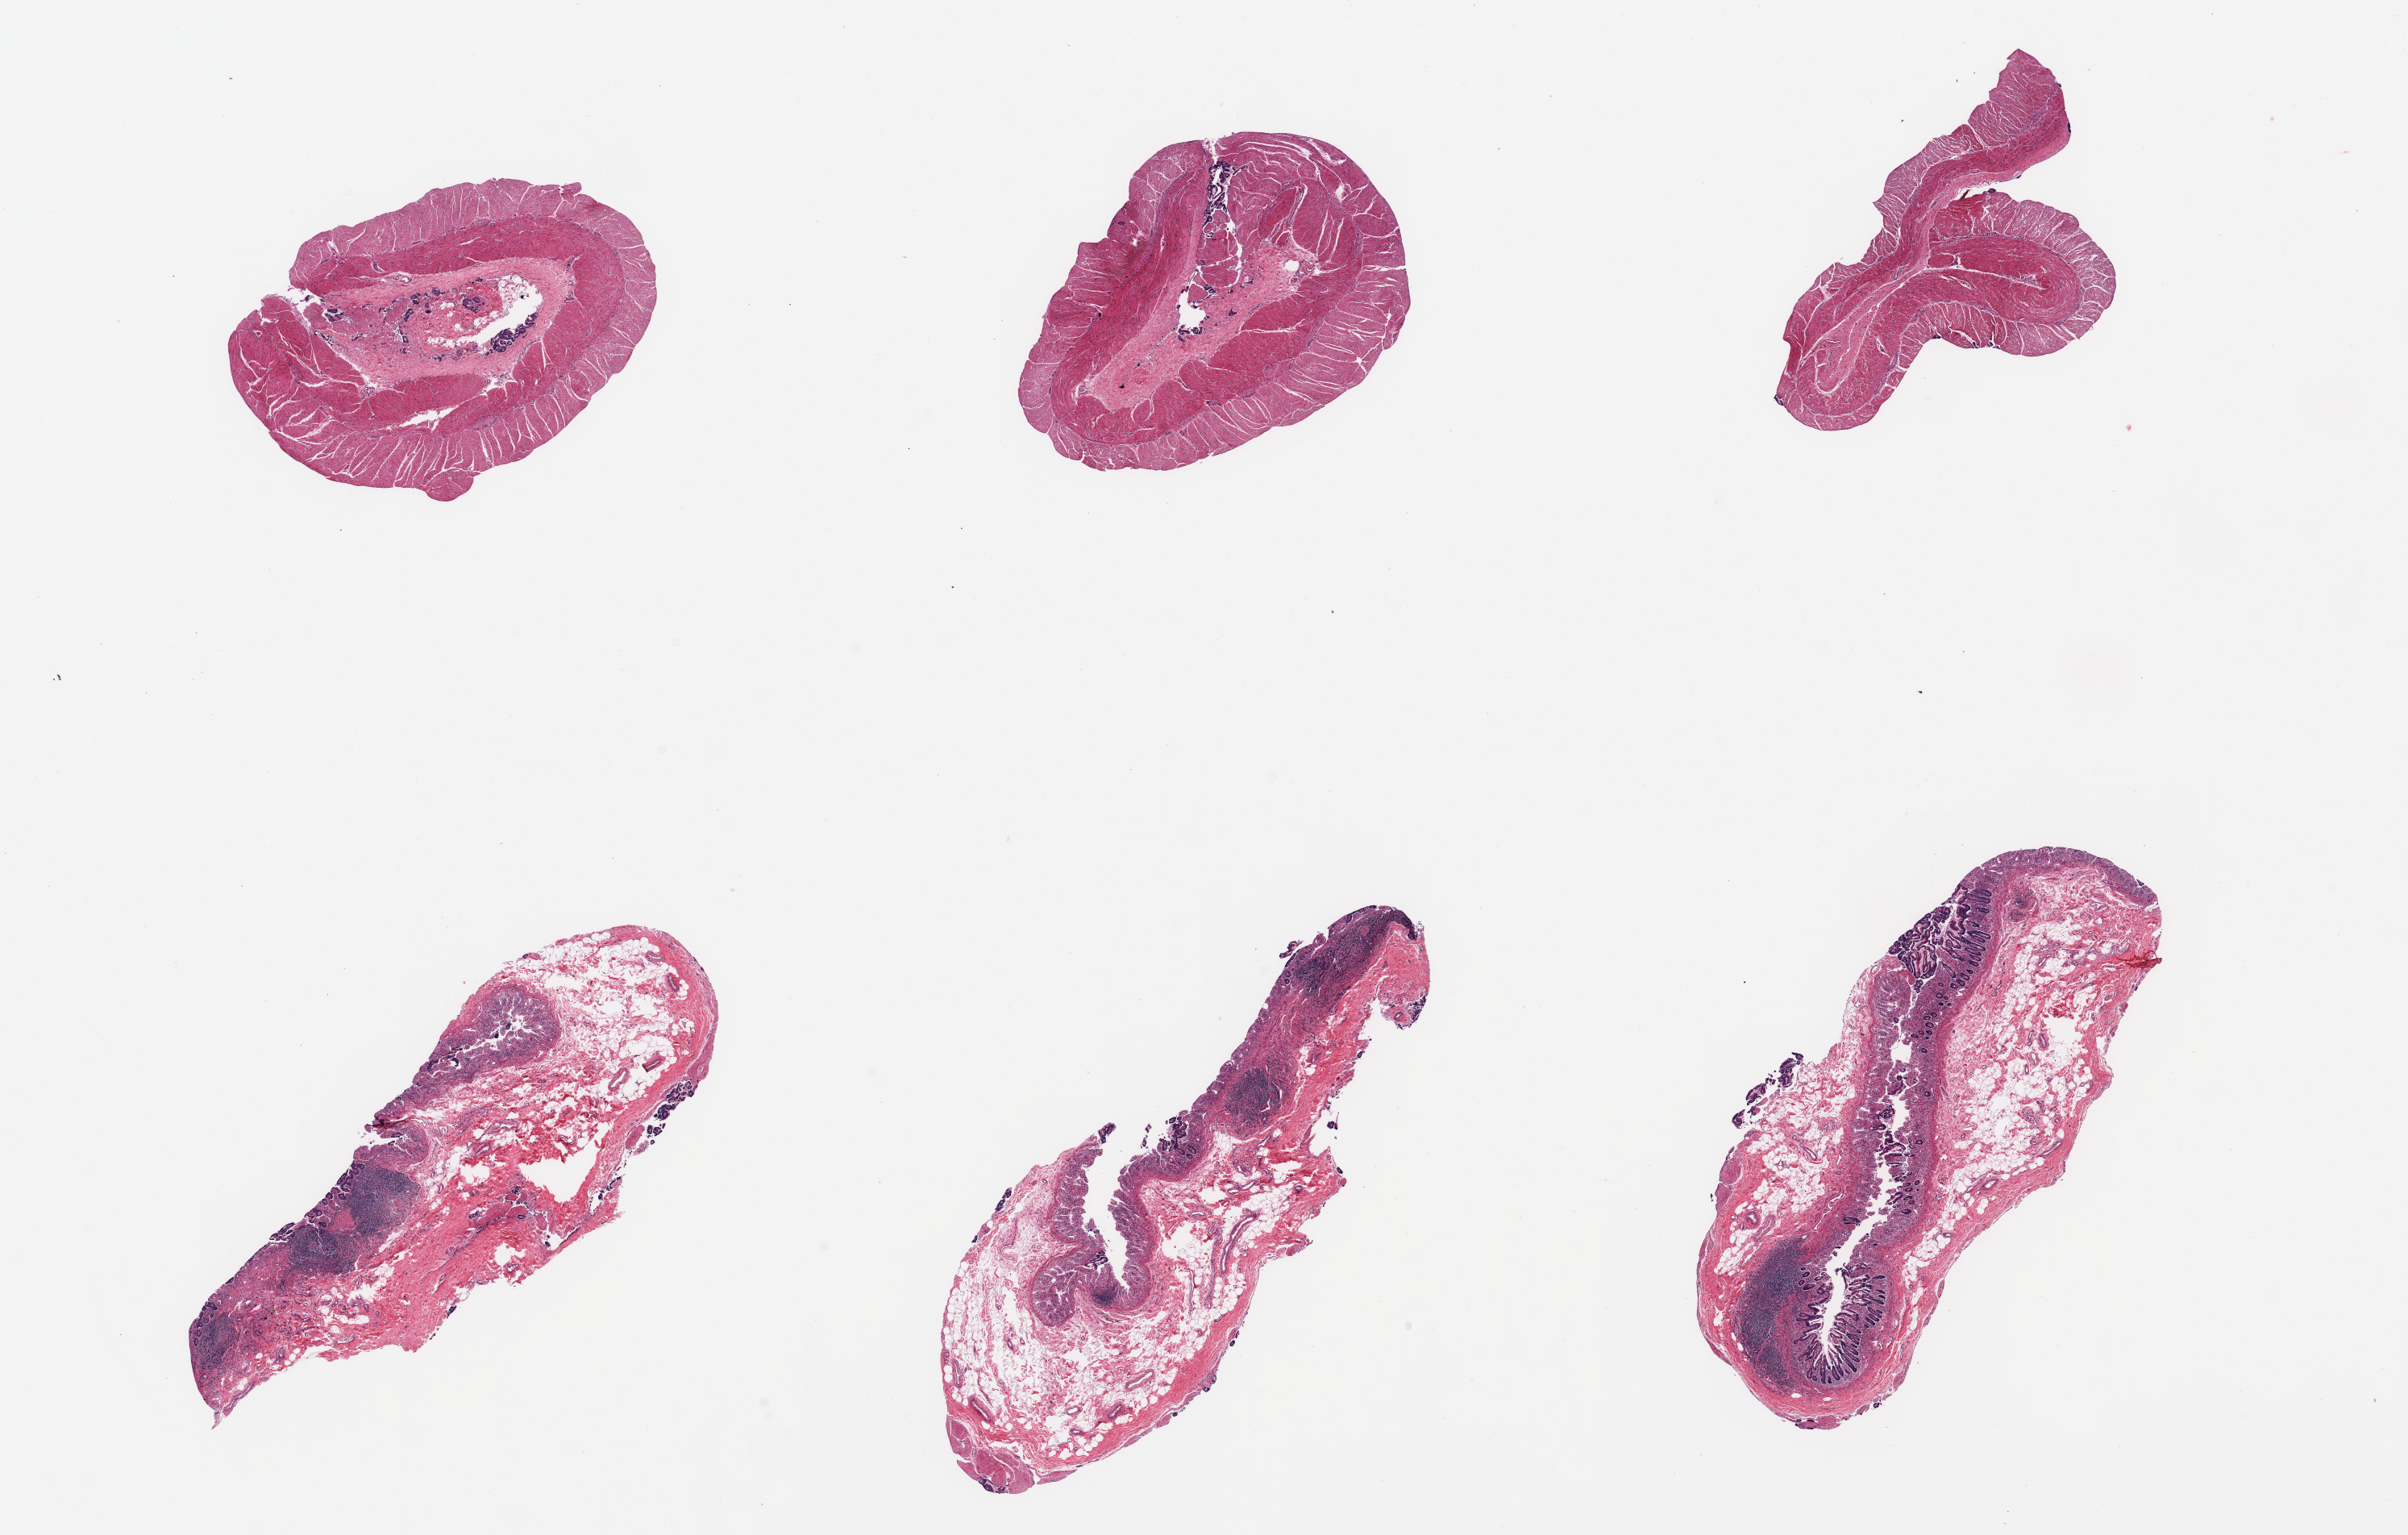
Digitized haematoxylin and eosin-stained section, low-resolution overview of the scanned area, about 23.6 x 15.1 mm; PAXgene-fixed, paraffin-embedded tissue; target tissue: ileum; donor tissue sample. Female donor.
- pathologist's review note for this sample: 6 pieces; 3 pieces mostly muscularis, not target; moderate to severe autolysis of mucosa; residual lymphoid aggregates are ~ 10 % of tissue